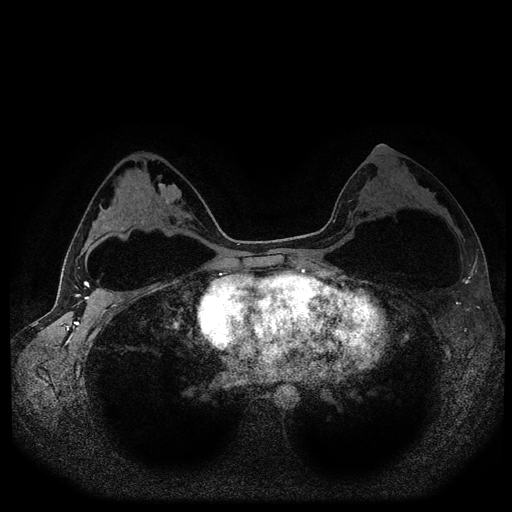
Breast MRI (dynamic contrast-enhanced, multi-phase), one axial slice; slice 63 of 116 in the series (ordered by position); dynamic contrast-enhanced series, time point 2 of 5 at this slice position (early post-contrast); 1.5 T; TE 2.6 ms, TR 5.4 ms; 2 mm slice thickness; 512 × 512 image matrix. Patient: female, 33 years.
Structures marked on this image (semi-automatically segmented with operator editing):
- breast lesion (labelled benign in the annotation): bounding box <158,183,181,207> (left, top, right, bottom; pixels)